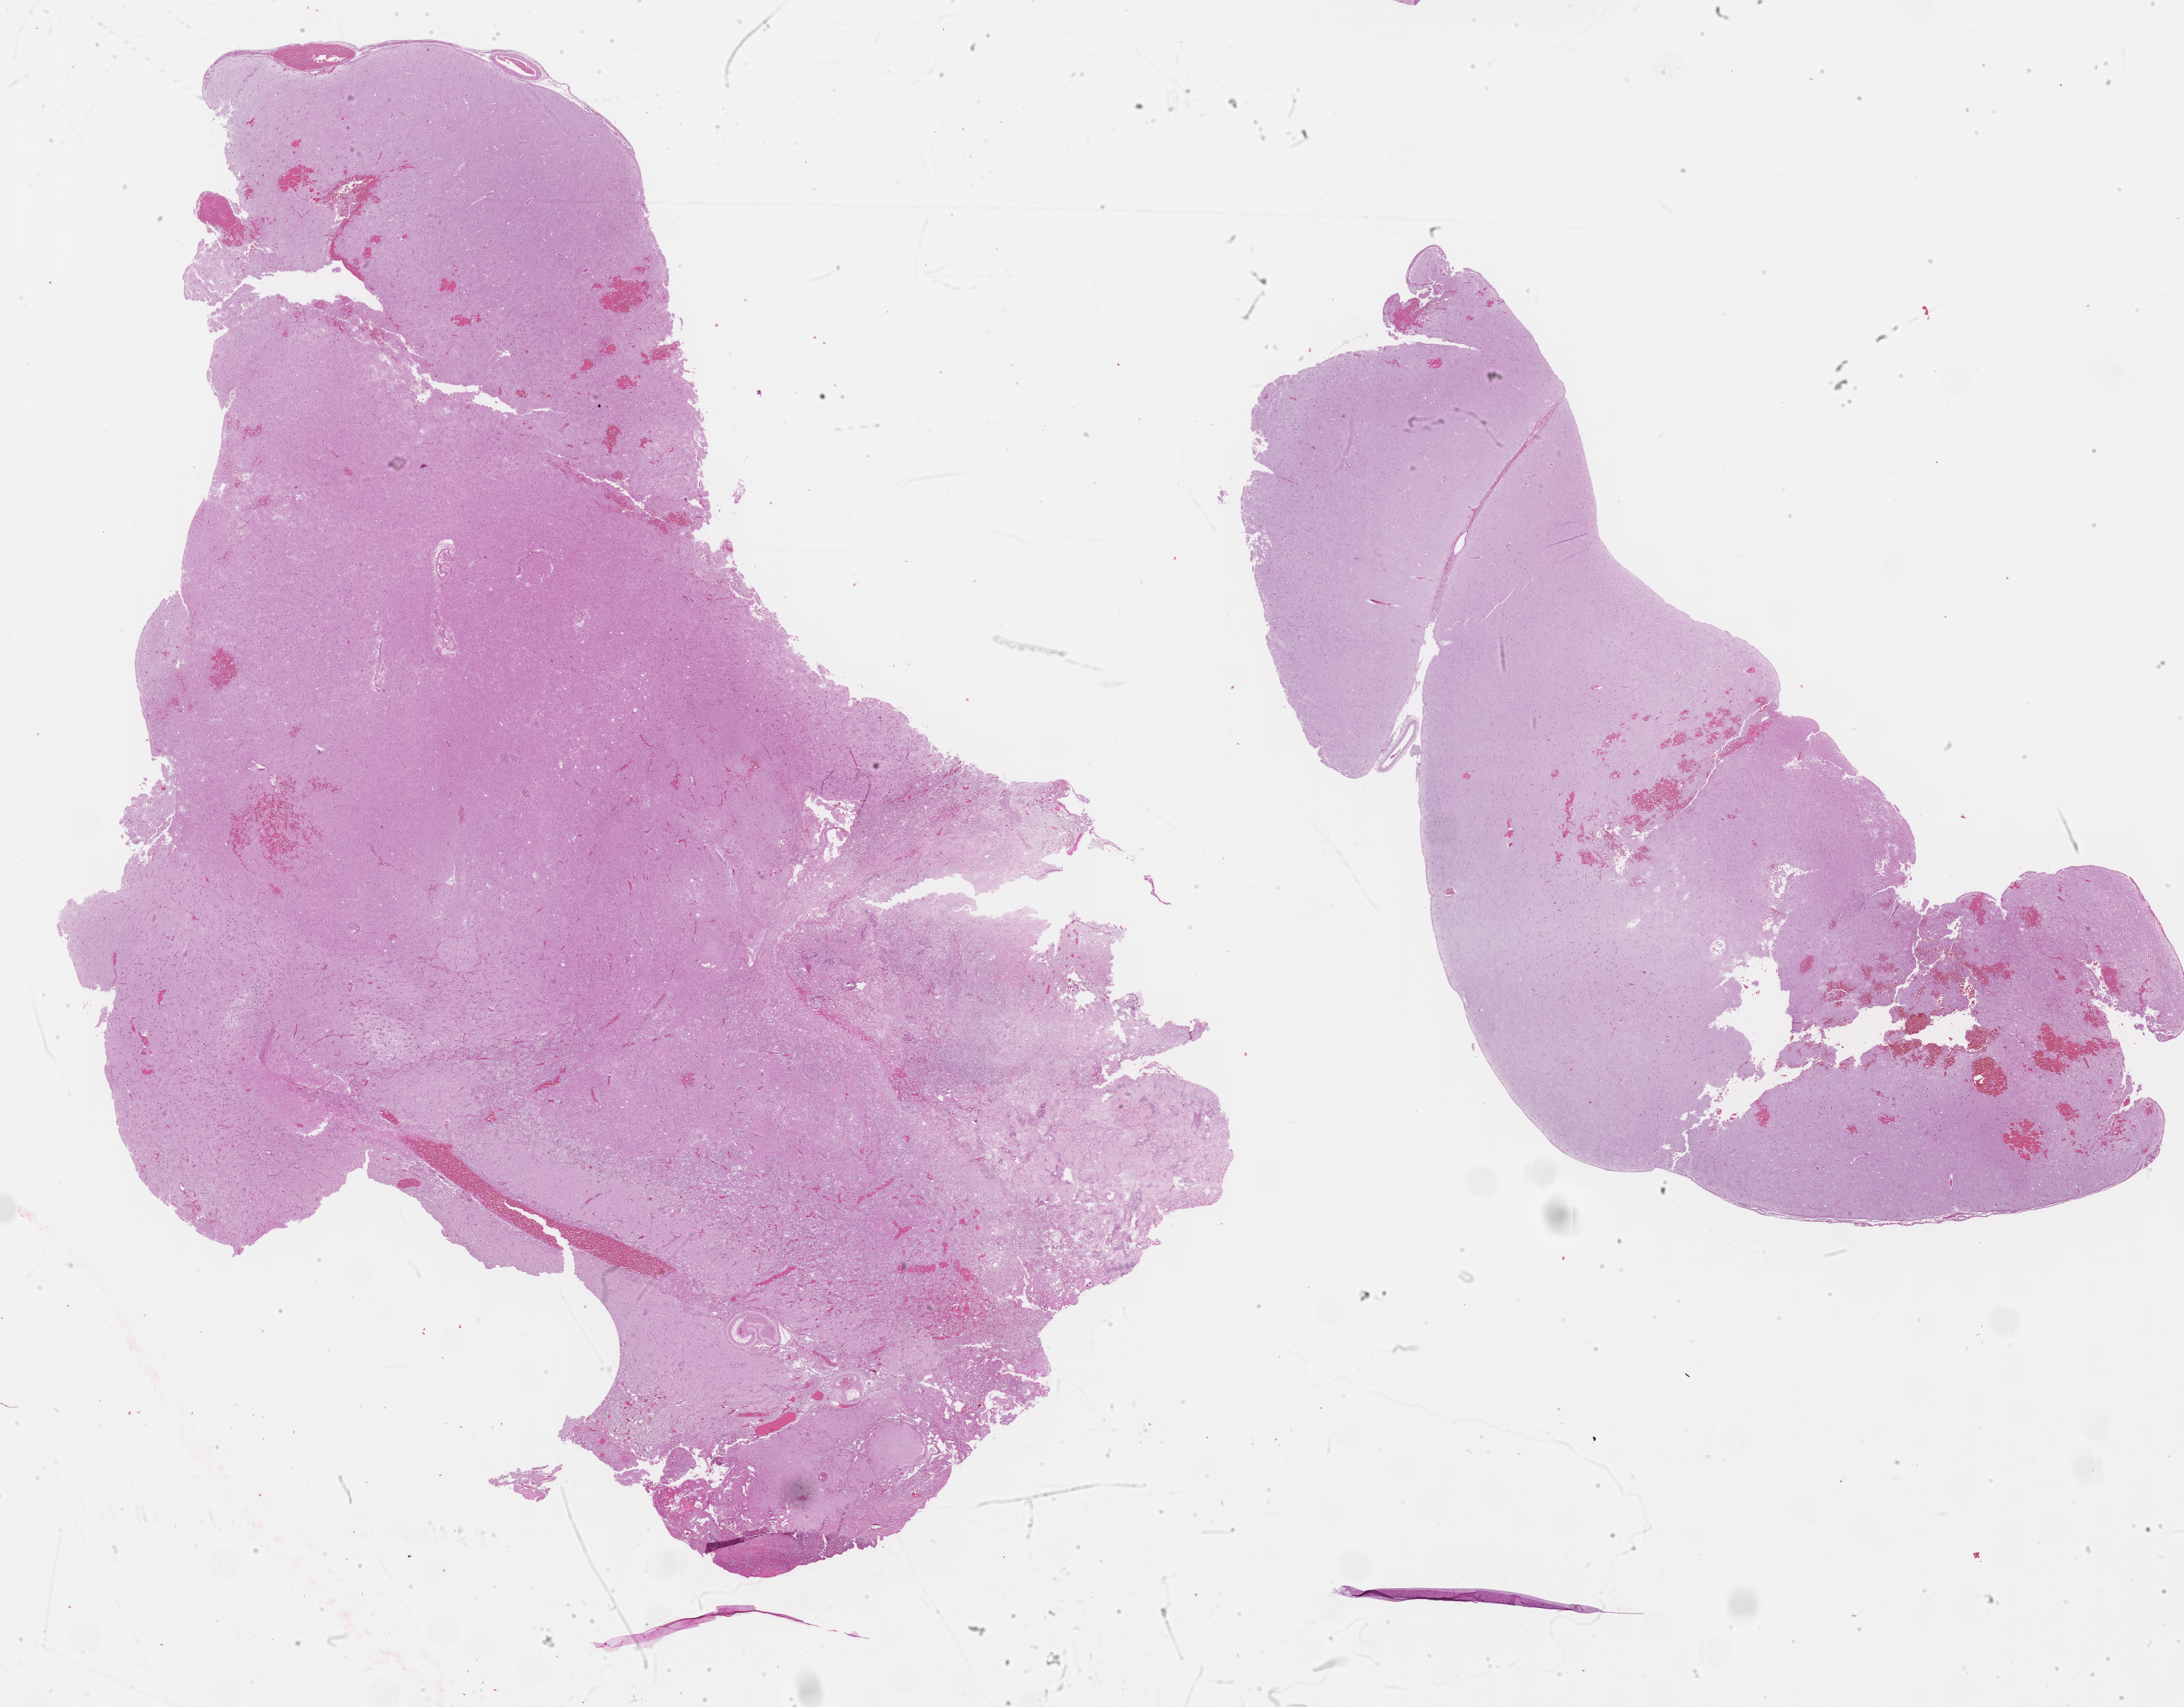
Digitized Hematoxylin and eosin (H&E) stained tissue section (whole slide) — whole scanned area (about 25.2 x 19.7 mm, acquisition: 40x scan) shown as a low-resolution overview; formalin-fixed paraffin-embedded (FFPE) diagnostic section; primary tumour sample from the brain. Patient: male, age at initial diagnosis 57 years.
* pathologic diagnosis: Glioblastoma